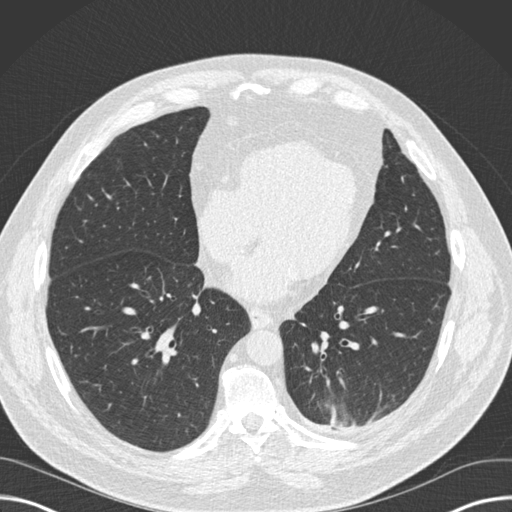
Low-dose screening chest CT, one axial slice. Slice 62 of 160 in the series (ordered by position). Reconstruction kernel B30f. Lung window (W 1500 / L -600 HU). 512 × 512 image matrix, field of view 382 × 382 mm.
Structures marked on this image (expert manual segmentation):
- lesion 1 (tumor, upper lobe of left lung): bounding box <330,406,346,427> (left, top, right, bottom; pixels)